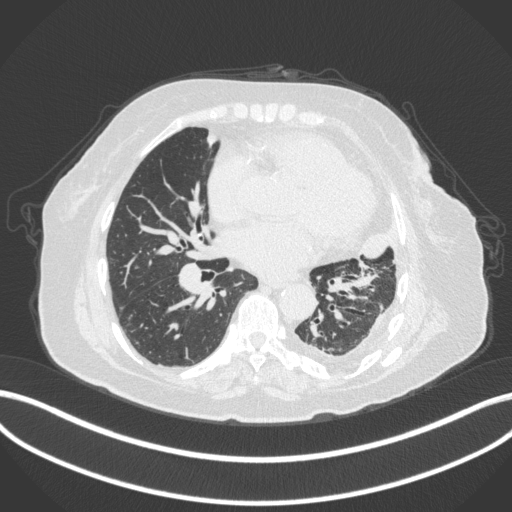
Chest CT, one axial slice. Slice 166 of 399 in the series (ordered by position). Reconstruction kernel B31f. 120 kVp. Lung window (W 1500 / L -600 HU). 1 mm slice thickness. 512 × 512 image matrix, field of view 400 × 400 mm. Female patient, age 75 years. From the clinical record (not read from this slice): clinical TNM (as recorded): T3 N3 M1.
Structures marked on this image (bounding box drawn by a radiologist):
- lung tumour (recorded histology: adenocarcinoma): box from (x=353, y=222) to (x=395, y=263) px